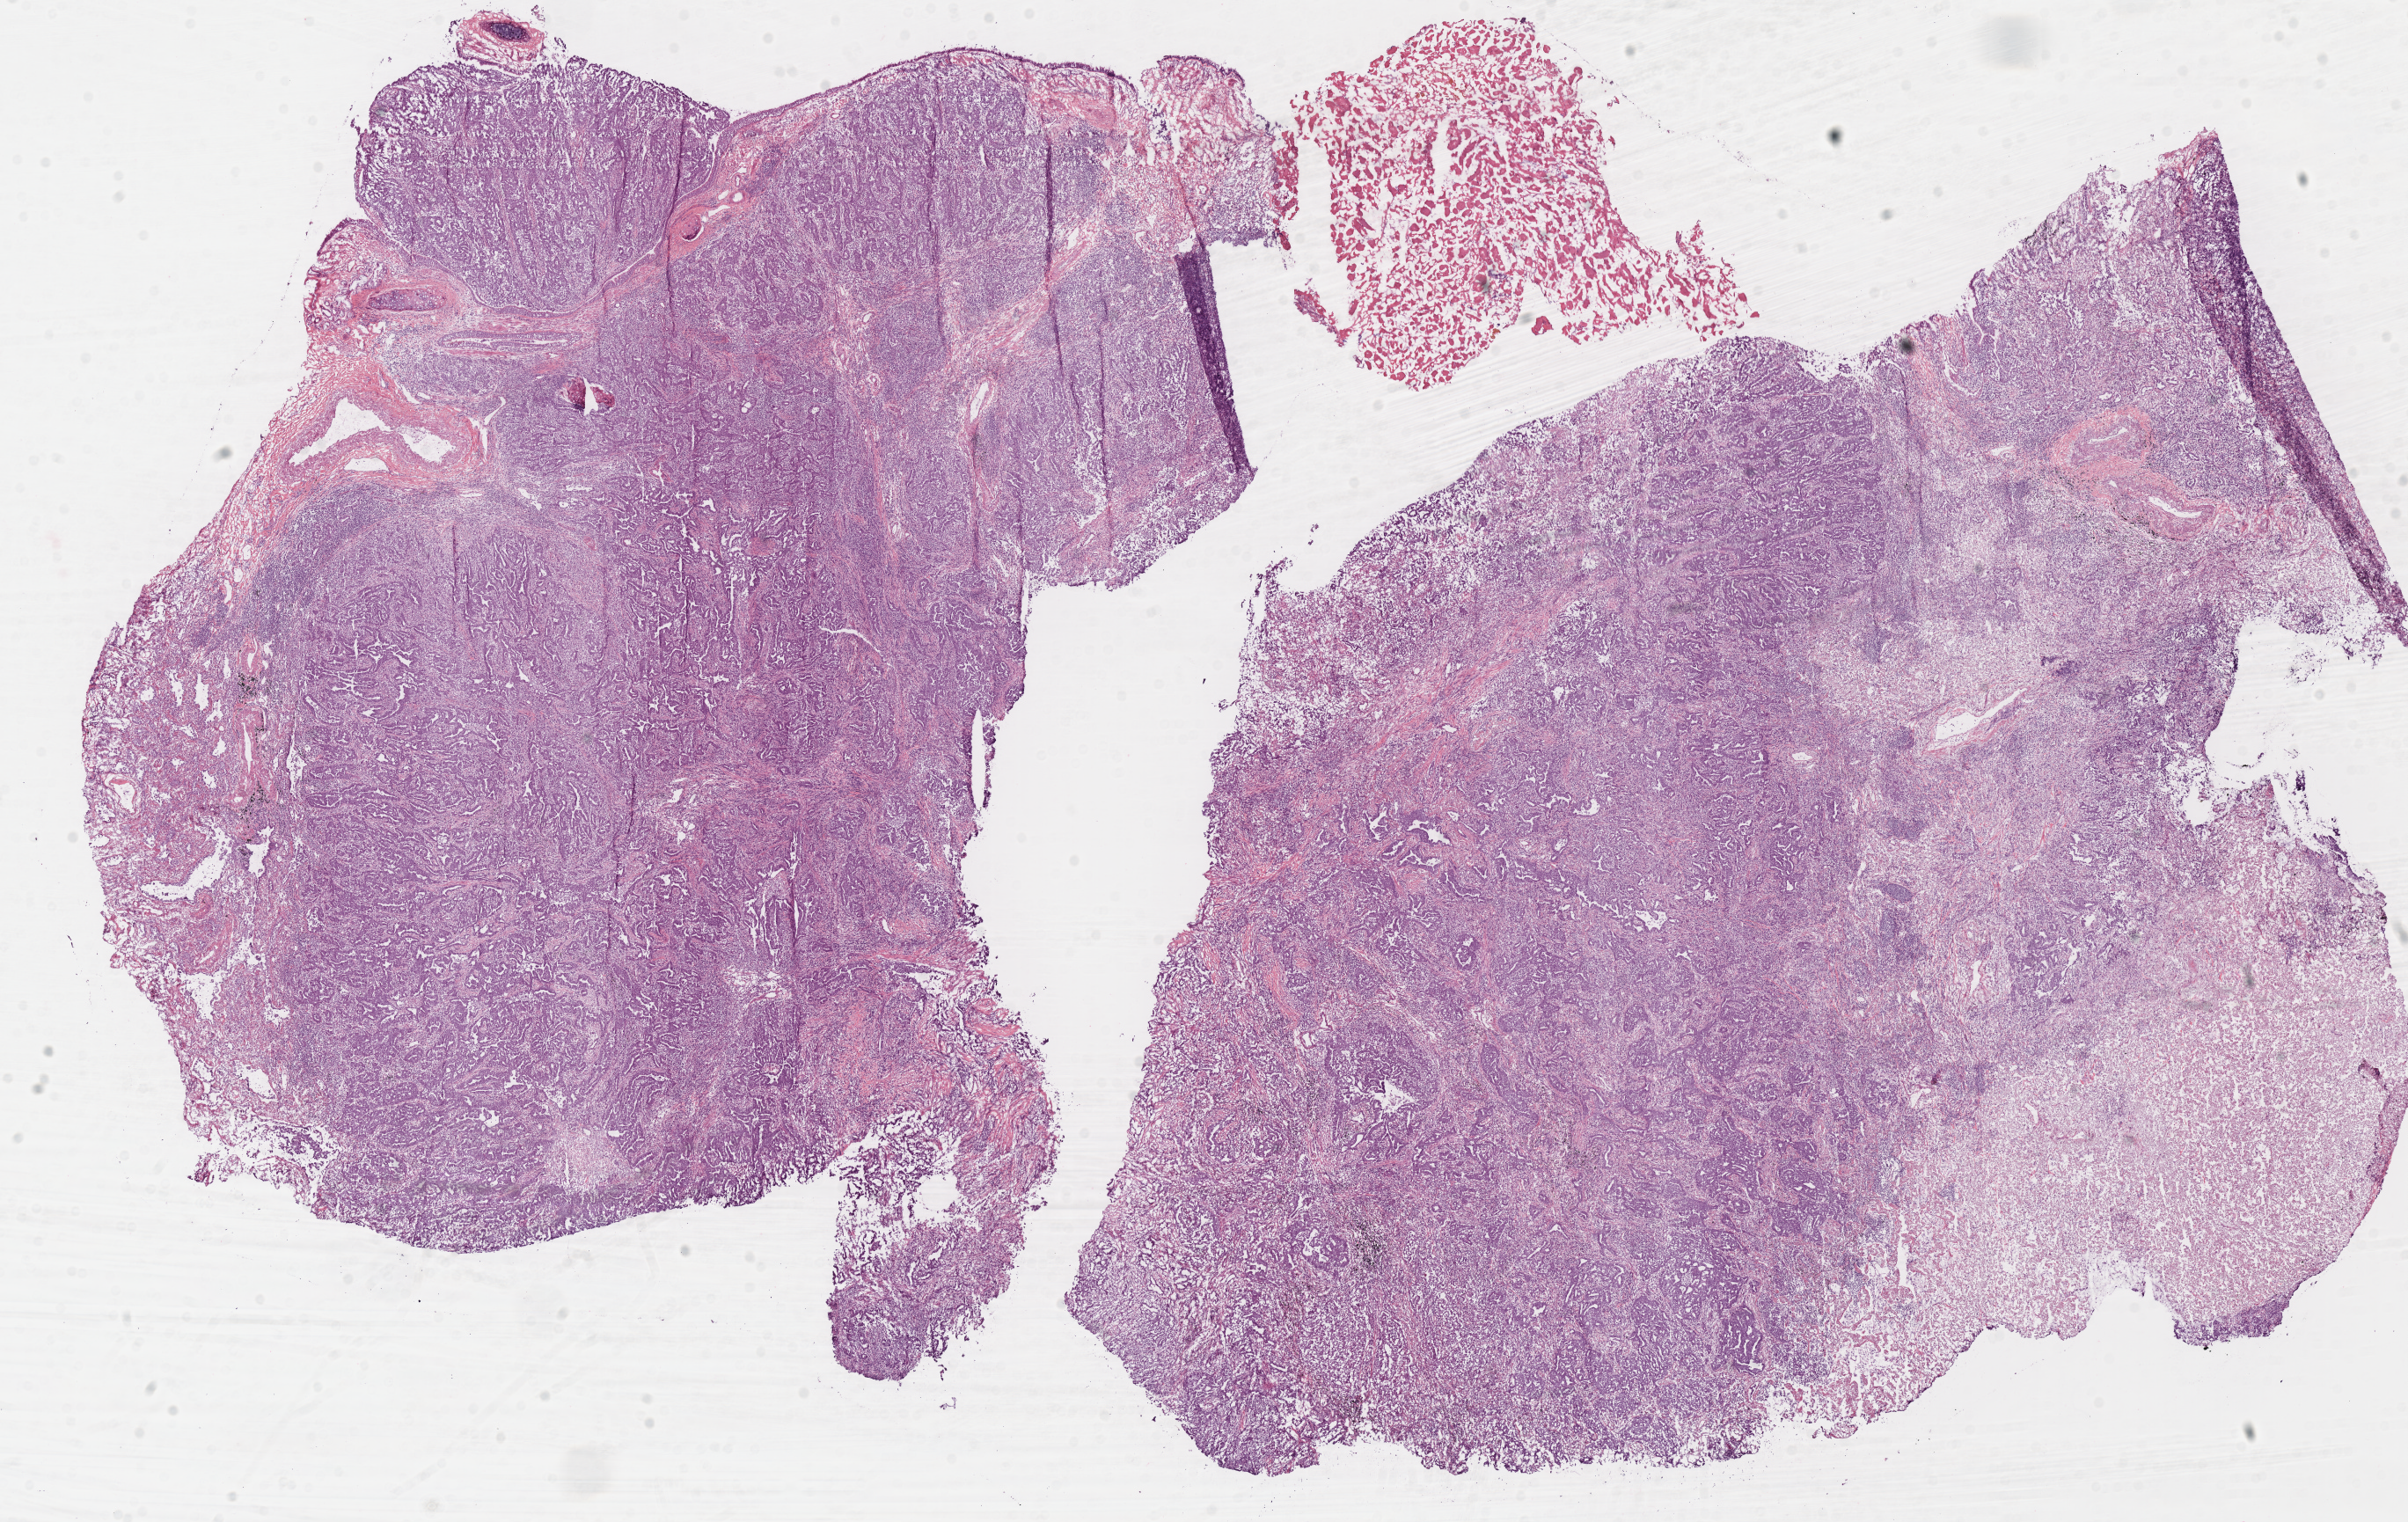
Digitized H&E tissue section (whole slide), low-resolution overview of the scanned area, about 21.6 x 13.6 mm, frozen section, sample: primary tumour, lung. Patient: female, age at initial diagnosis 81 years. Pathologist review of this section (percent, as recorded): tumour cells 75%, tumour nuclei 65%, normal cells 20%, stromal cells 5%, necrosis 0%. Inflammatory infiltration, as recorded: lymphocyte infiltration 20%, monocyte infiltration 2%, neutrophil infiltration 0%.
AJCC pathologic stage: IB (7th edition). Histologic diagnosis: Adenocarcinoma with mixed subtypes (upper lobe, lung).